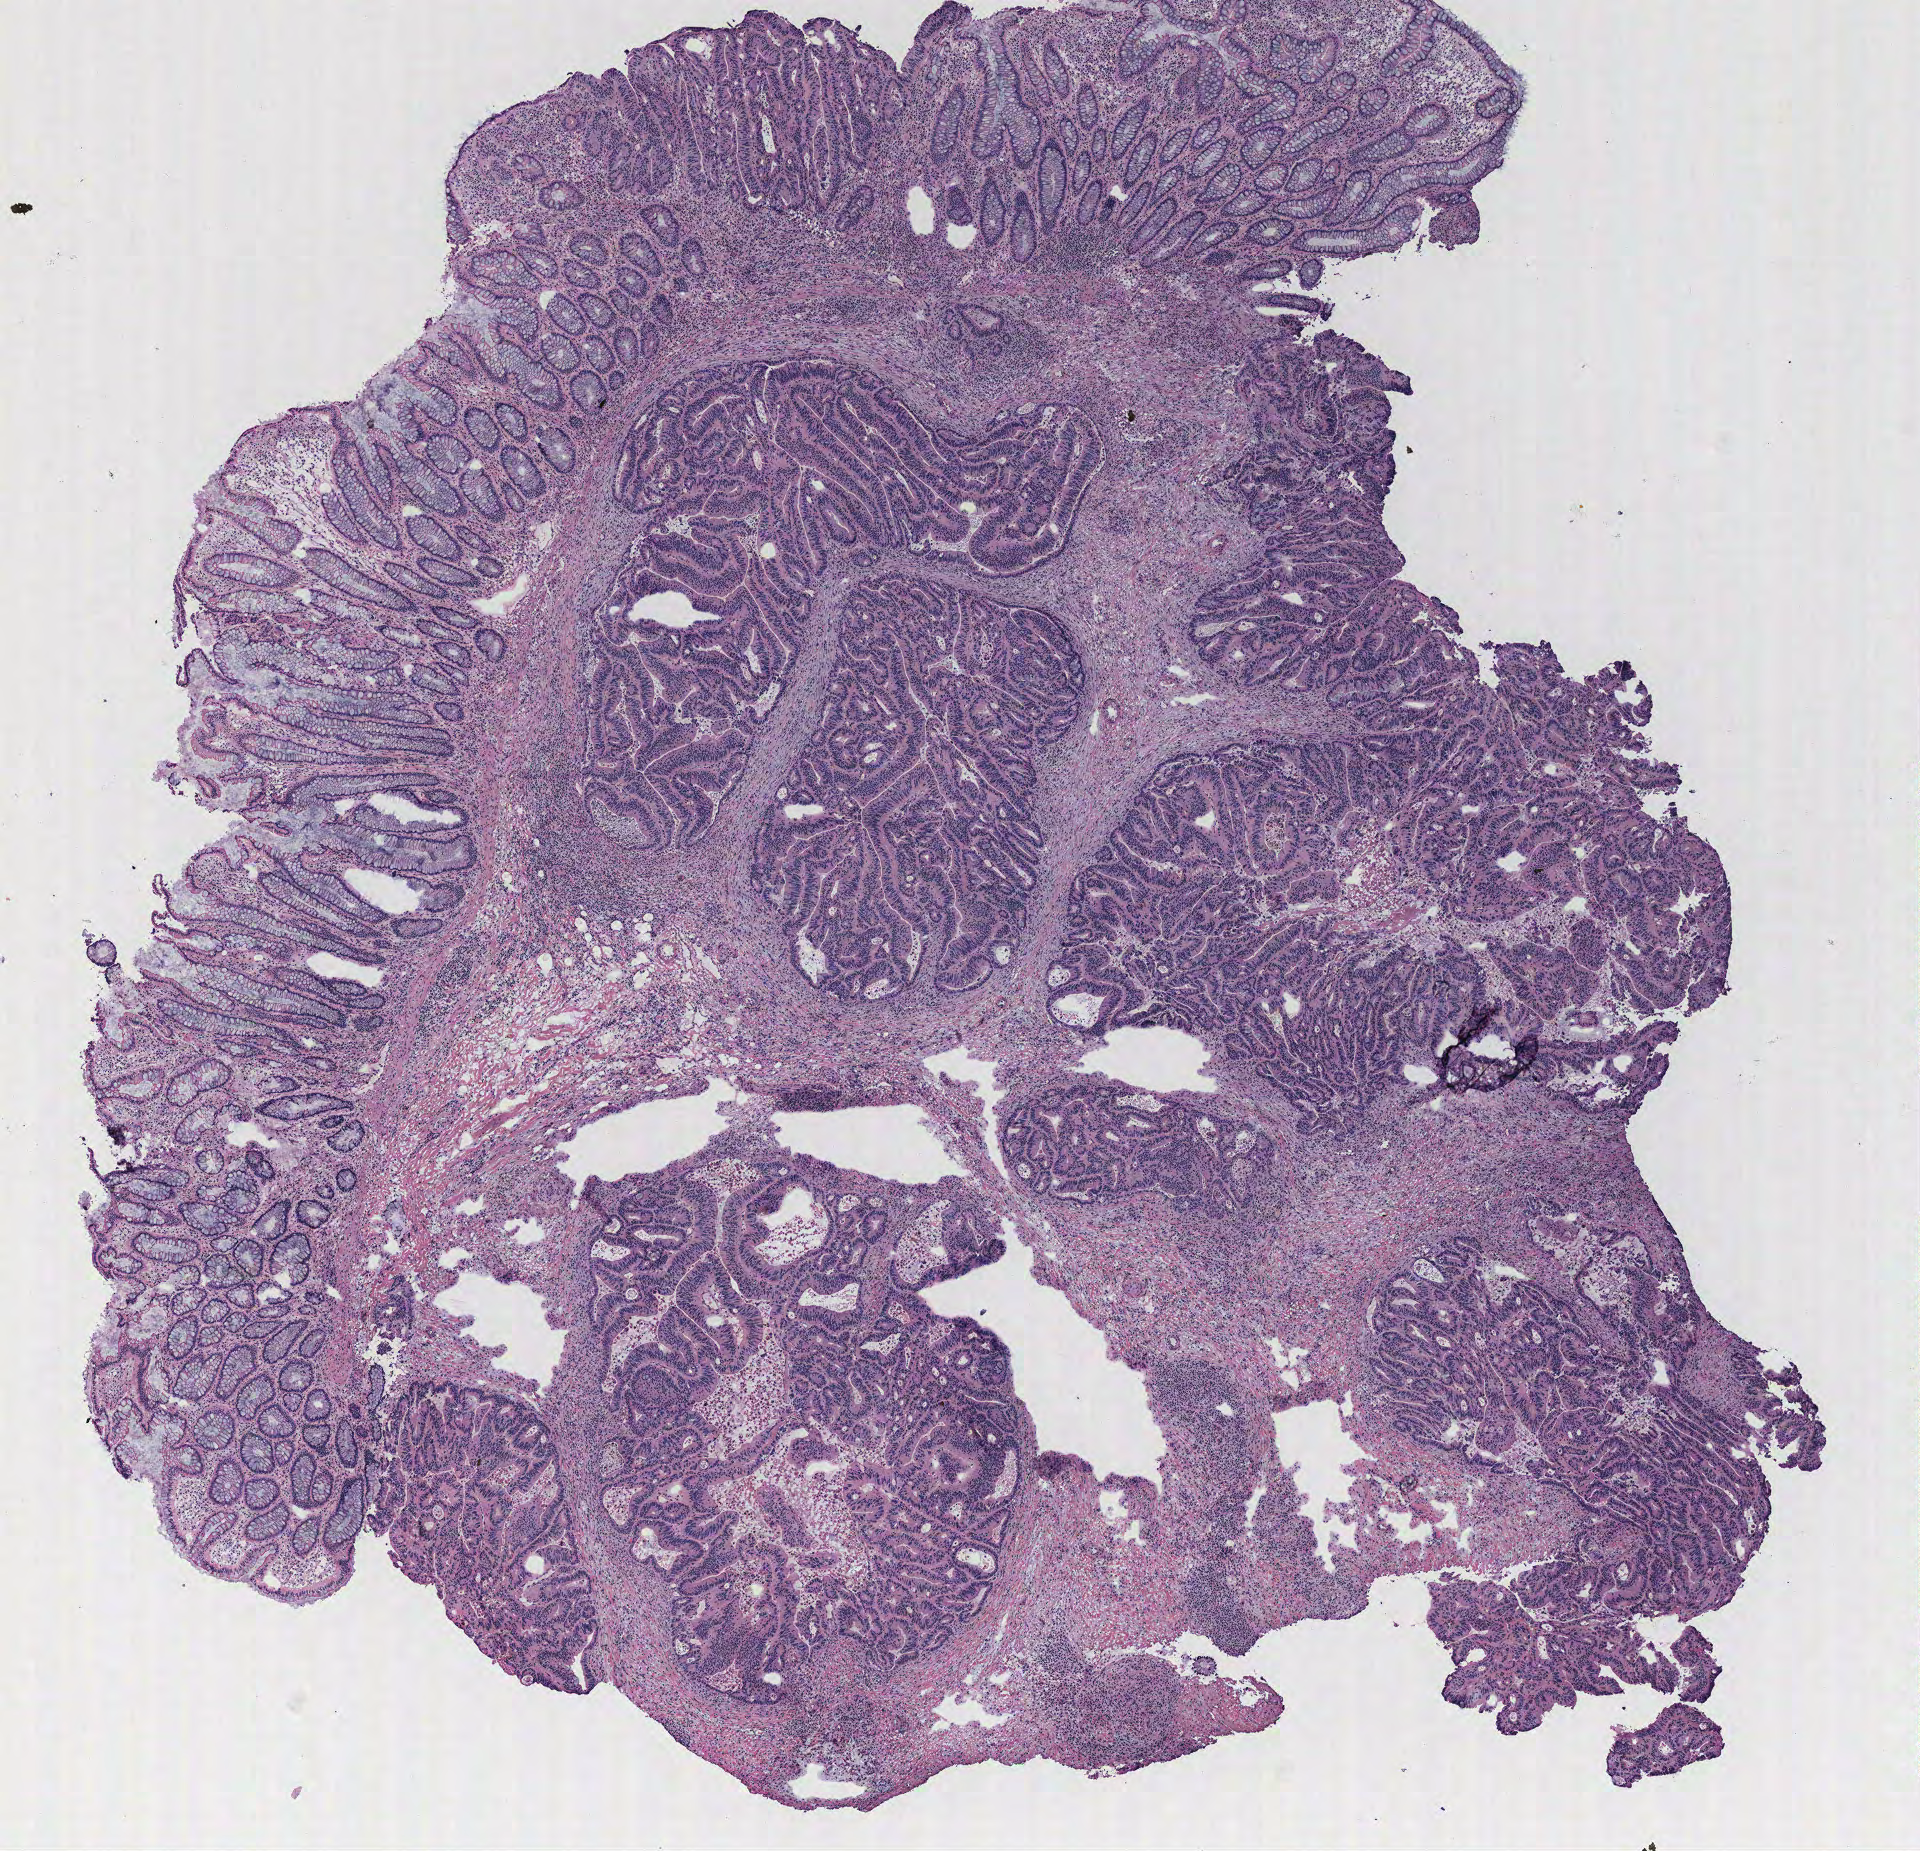
Hematoxylin and eosin (H&E) stained whole-slide image — a low-resolution overview of the entire scanned area, about 7.7 x 7.4 mm (from a 40x scan); colon, tumour tissue. Patient: male, age 54 years.
- primary tumour site (as recorded): colon
- AJCC pathologic stage: IIA
- histologic diagnosis: Adenocarcinoma, NOS